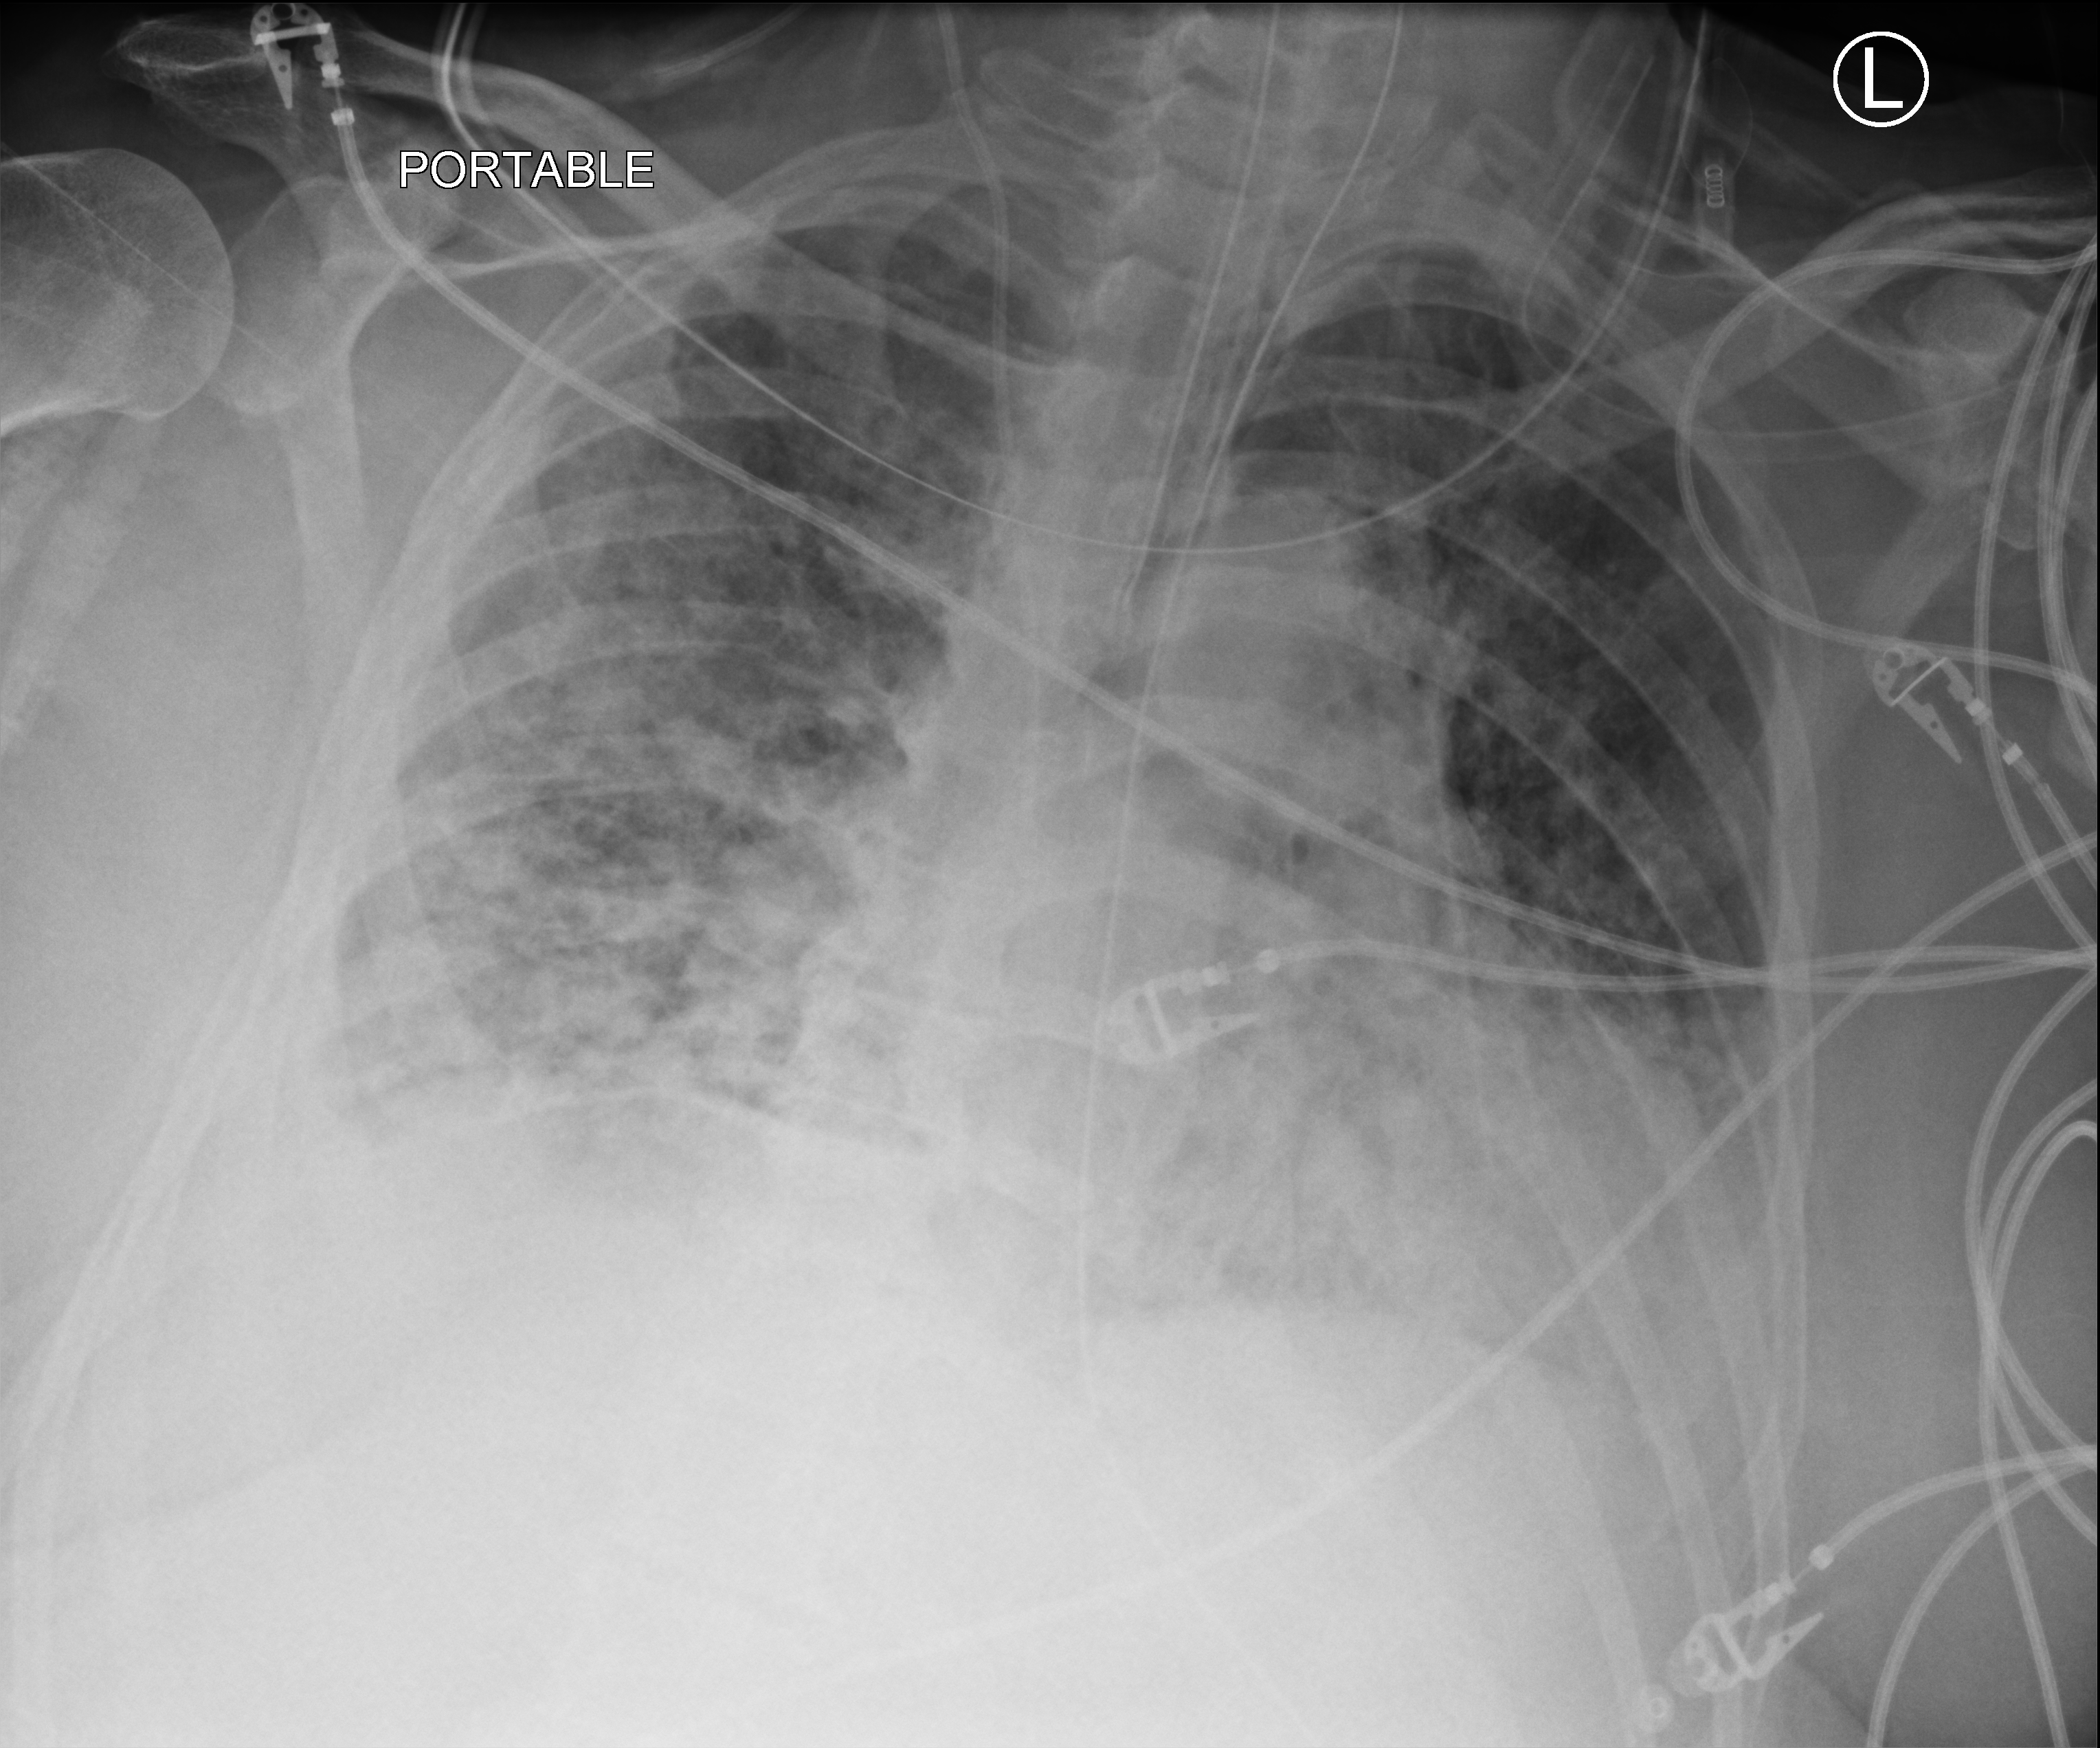
Chest X-ray (portable); anteroposterior (AP) projection. Male patient hospitalised with COVID-19, age 60–74 years.
Admission-level facts for this patient (not findings on this image; timing relative to this image not recorded):
- admitted to intensive care during this hospital stay: yes
- hypertension (admission record): yes